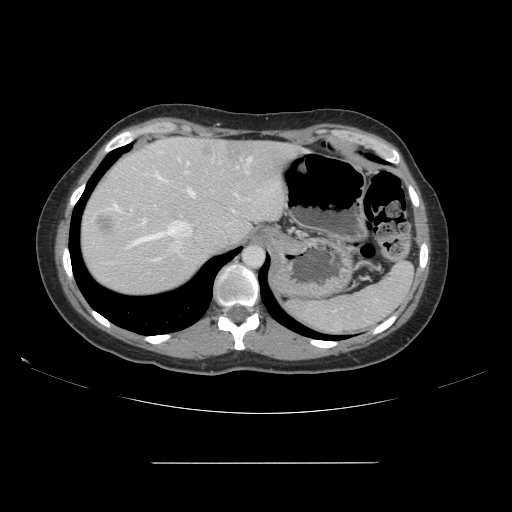
Contrast-enhanced abdominal CT, one axial slice. 120 kVp. Intravenous contrast given. Soft-tissue window (W 400 / L 40 HU). 2.5 mm slice thickness. 512 × 512 image matrix, field of view 421 × 421 mm. Female patient, age 46 years. Case-level facts recorded for this patient, not image findings: diagnosis: colorectal cancer liver metastases, imaged before liver resection; multiple liver metastases: yes; largest metastasis: 3 cm; chemotherapy before resection: no.
Annotated regions visible in this slice (outlined manually by an expert reader):
- hepatic veins: bounding box (x1, y1, x2, y2) in pixels: (109, 157, 253, 250)
- liver: (81, 138, 296, 295)
- planned liver remnant (the part of the liver to remain after resection): (93, 139, 297, 248)
- portal vein (with intrahepatic branches): (232, 194, 237, 212)
- liver metastasis: (96, 216, 113, 233)
- liver metastasis: (204, 148, 212, 155)